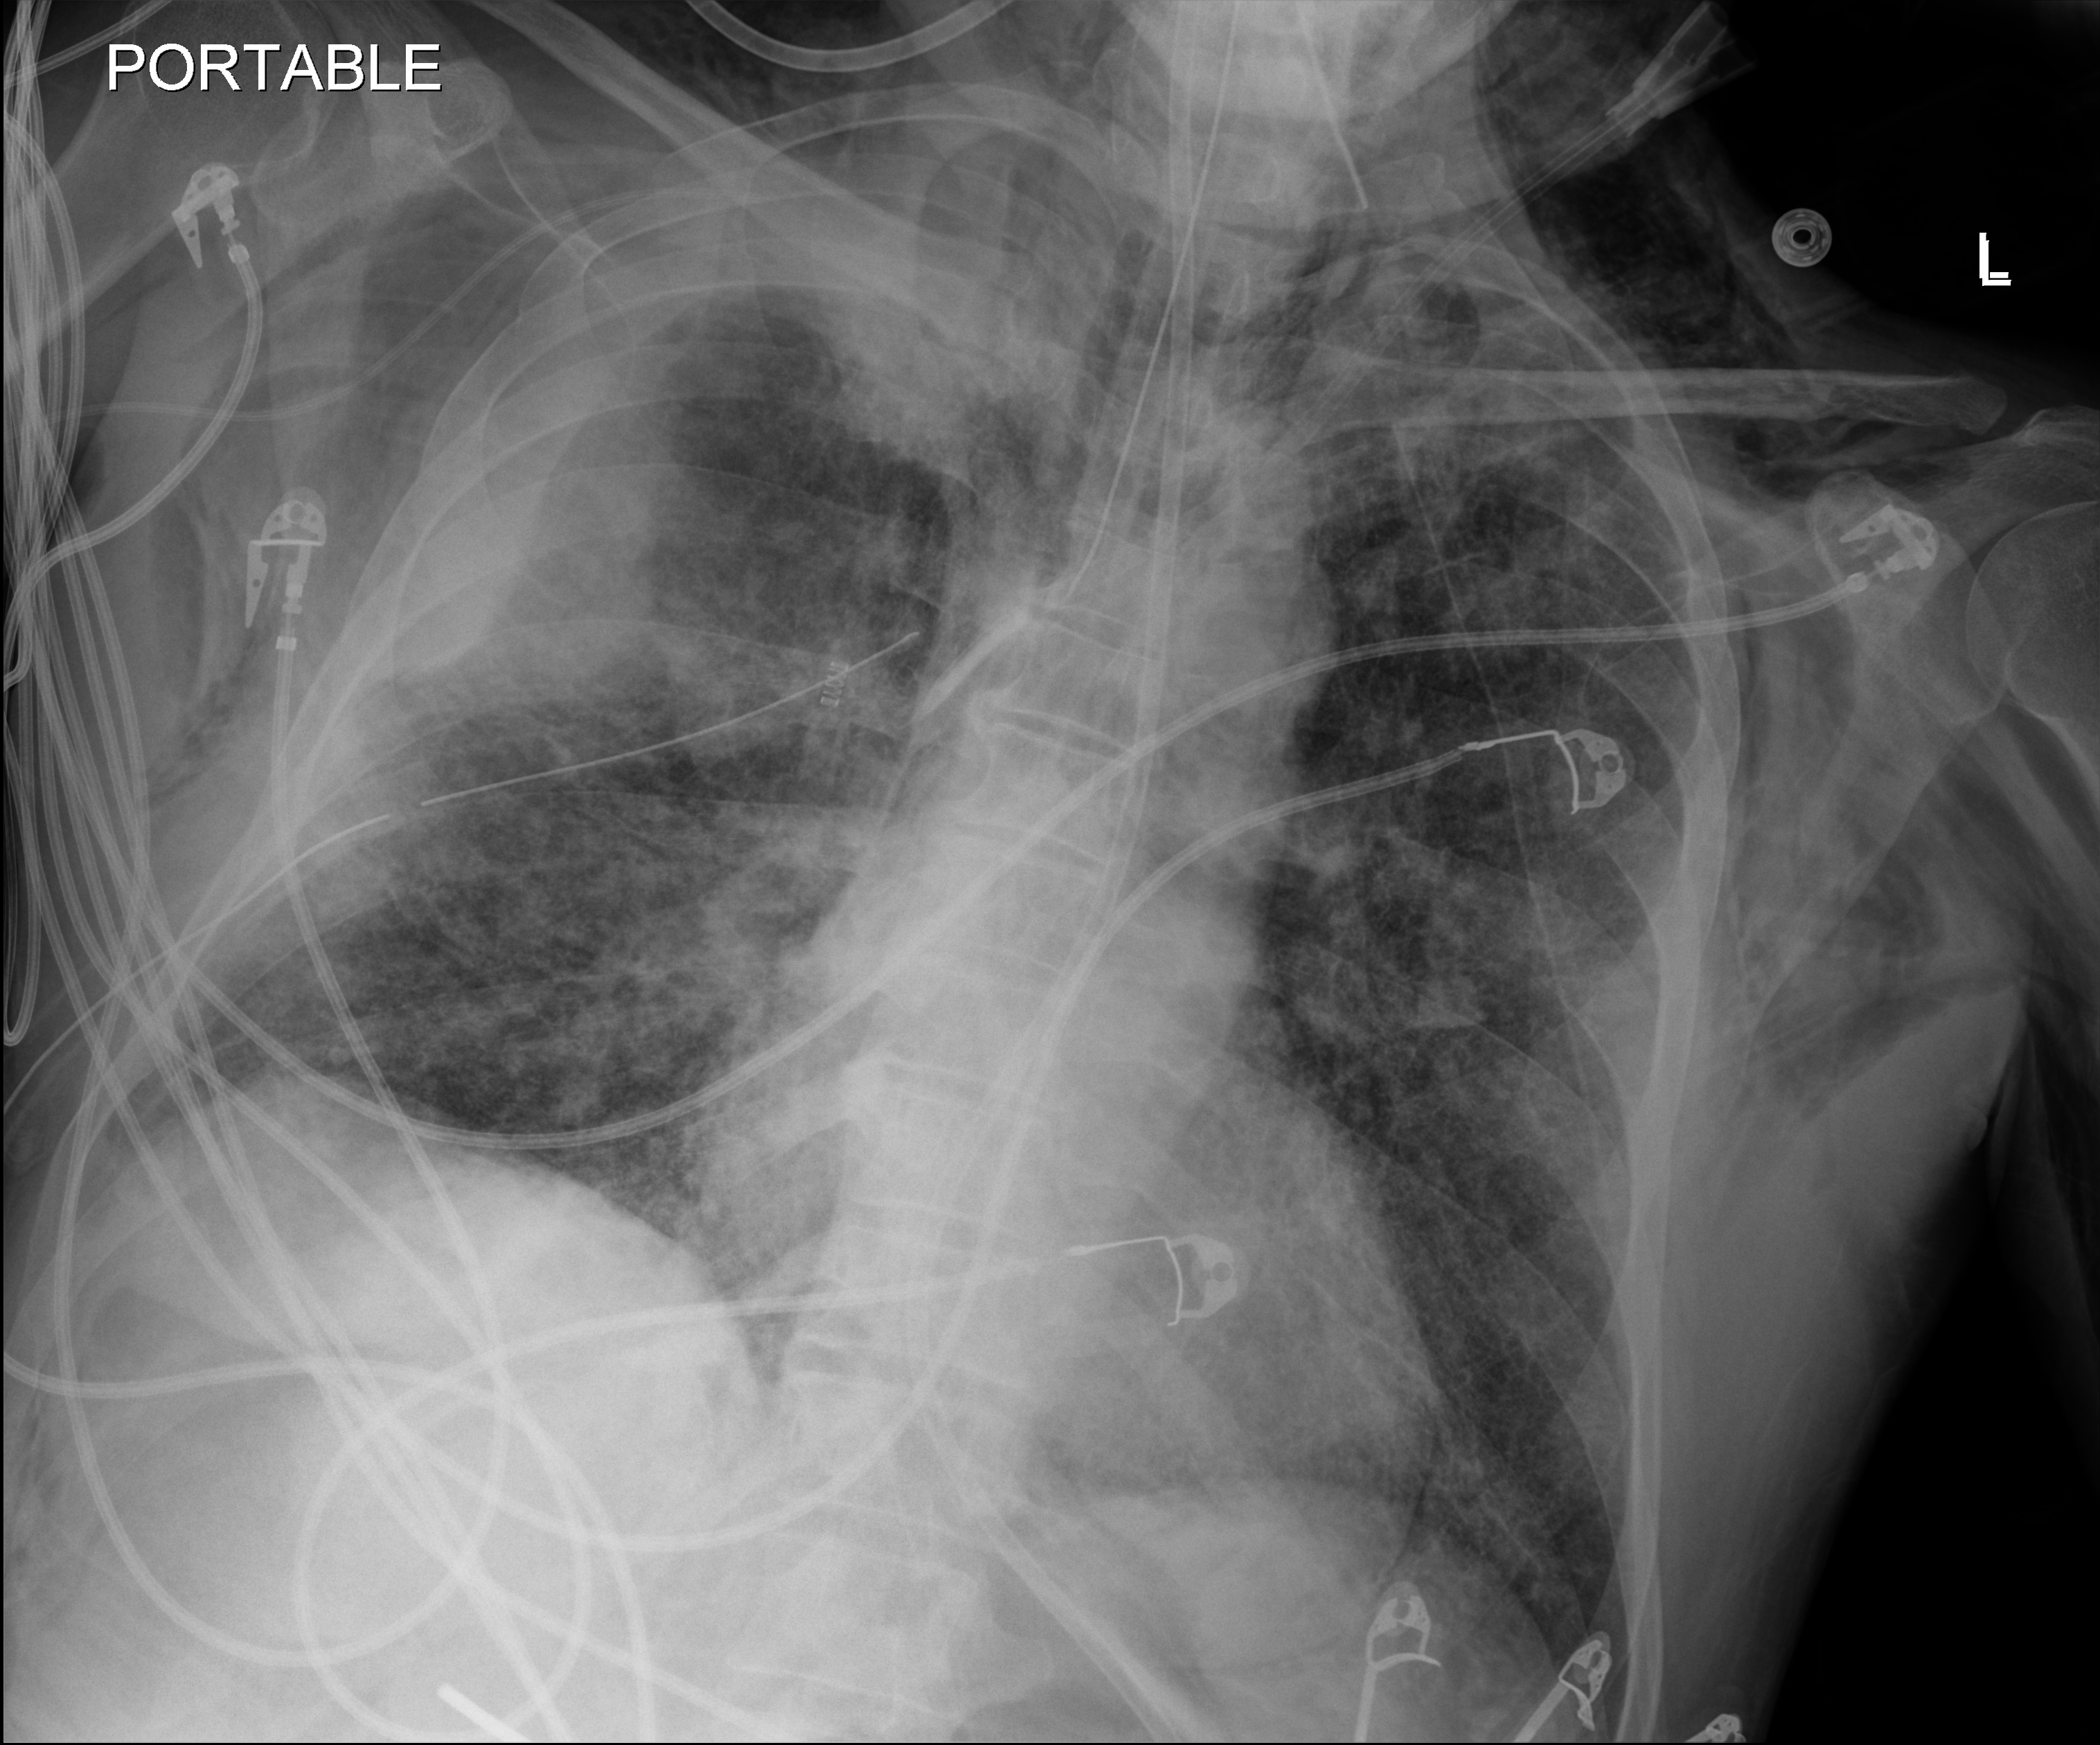
Bedside chest radiograph (digital radiography); anteroposterior (AP) projection. Male patient hospitalised with COVID-19, age 18–59 years.
Hospital-stay facts (about this admission, not read from this image; timing relative to this image not recorded):
- admitted to intensive care during this hospital stay: yes